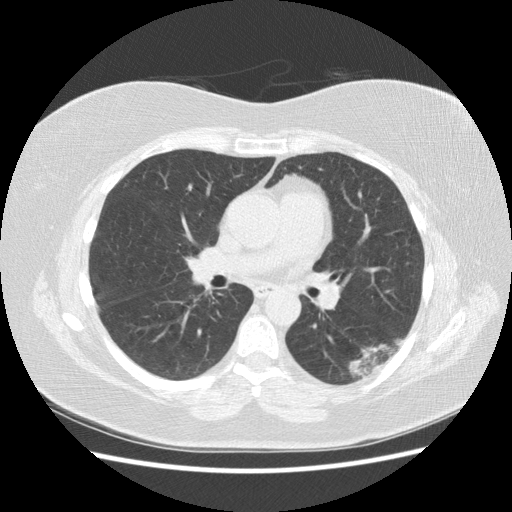
Axial slice from a low-dose chest CT screening exam. Third screening round (two years after baseline). Lung window (W 1500 / L -600 HU). 2.5 mm slice thickness. Standard (soft-tissue) reconstruction kernel (STANDARD). Slice 85 of 151 in the series. Female participant, aged 57 years at enrolment. Current smoker at enrolment.
Expert reader's lesion annotation, bounding box <331,325,411,387> (left, top, right, bottom; pixels). Screening reader's record for this exam (one nodule recorded; not confirmed to be the boxed lesion): non-calcified nodule or mass ≥4 mm, left lower lobe, 40 × 20 mm, poorly defined margins, mixed attenuation, pre-existing on the prior screen: yes; interval growth: yes. Later outcome: lung cancer diagnosed 55 days after this screen — squamous cell carcinoma, NOS, left lower lobe, poorly differentiated (G3), stage IB (AJCC 6th edition), 40 mm at pathology.